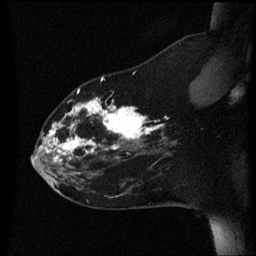
Breast MRI (dynamic contrast-enhanced), one sagittal slice; slice 18 of 60 in the series (ordered by position); dynamic contrast-enhanced series, image 2 of 3 at this slice position (ordered by acquisition); 1.5 T; TE 4.2 ms, TR 8.4 ms; 2.2 mm slice thickness; 256 × 256 image matrix, field of view 200 × 200 mm. Female patient, age 35 years. Case-level facts recorded for this patient, not image findings: setting: breast cancer imaged before/during neoadjuvant chemotherapy; receptor status: HER2-positive.
Structures marked on this image (semi-automatic segmentation, software-assisted and operator-edited):
- analysis volume of interest (the breast-tissue region the enhancement analysis was run in; not a lesion): bounding box [x1, y1, x2, y2] px = [32, 74, 178, 173]
- tumour enhancement mask (voxels above the 70 % enhancement threshold inside the analysis volume of interest): [39, 76, 165, 161]